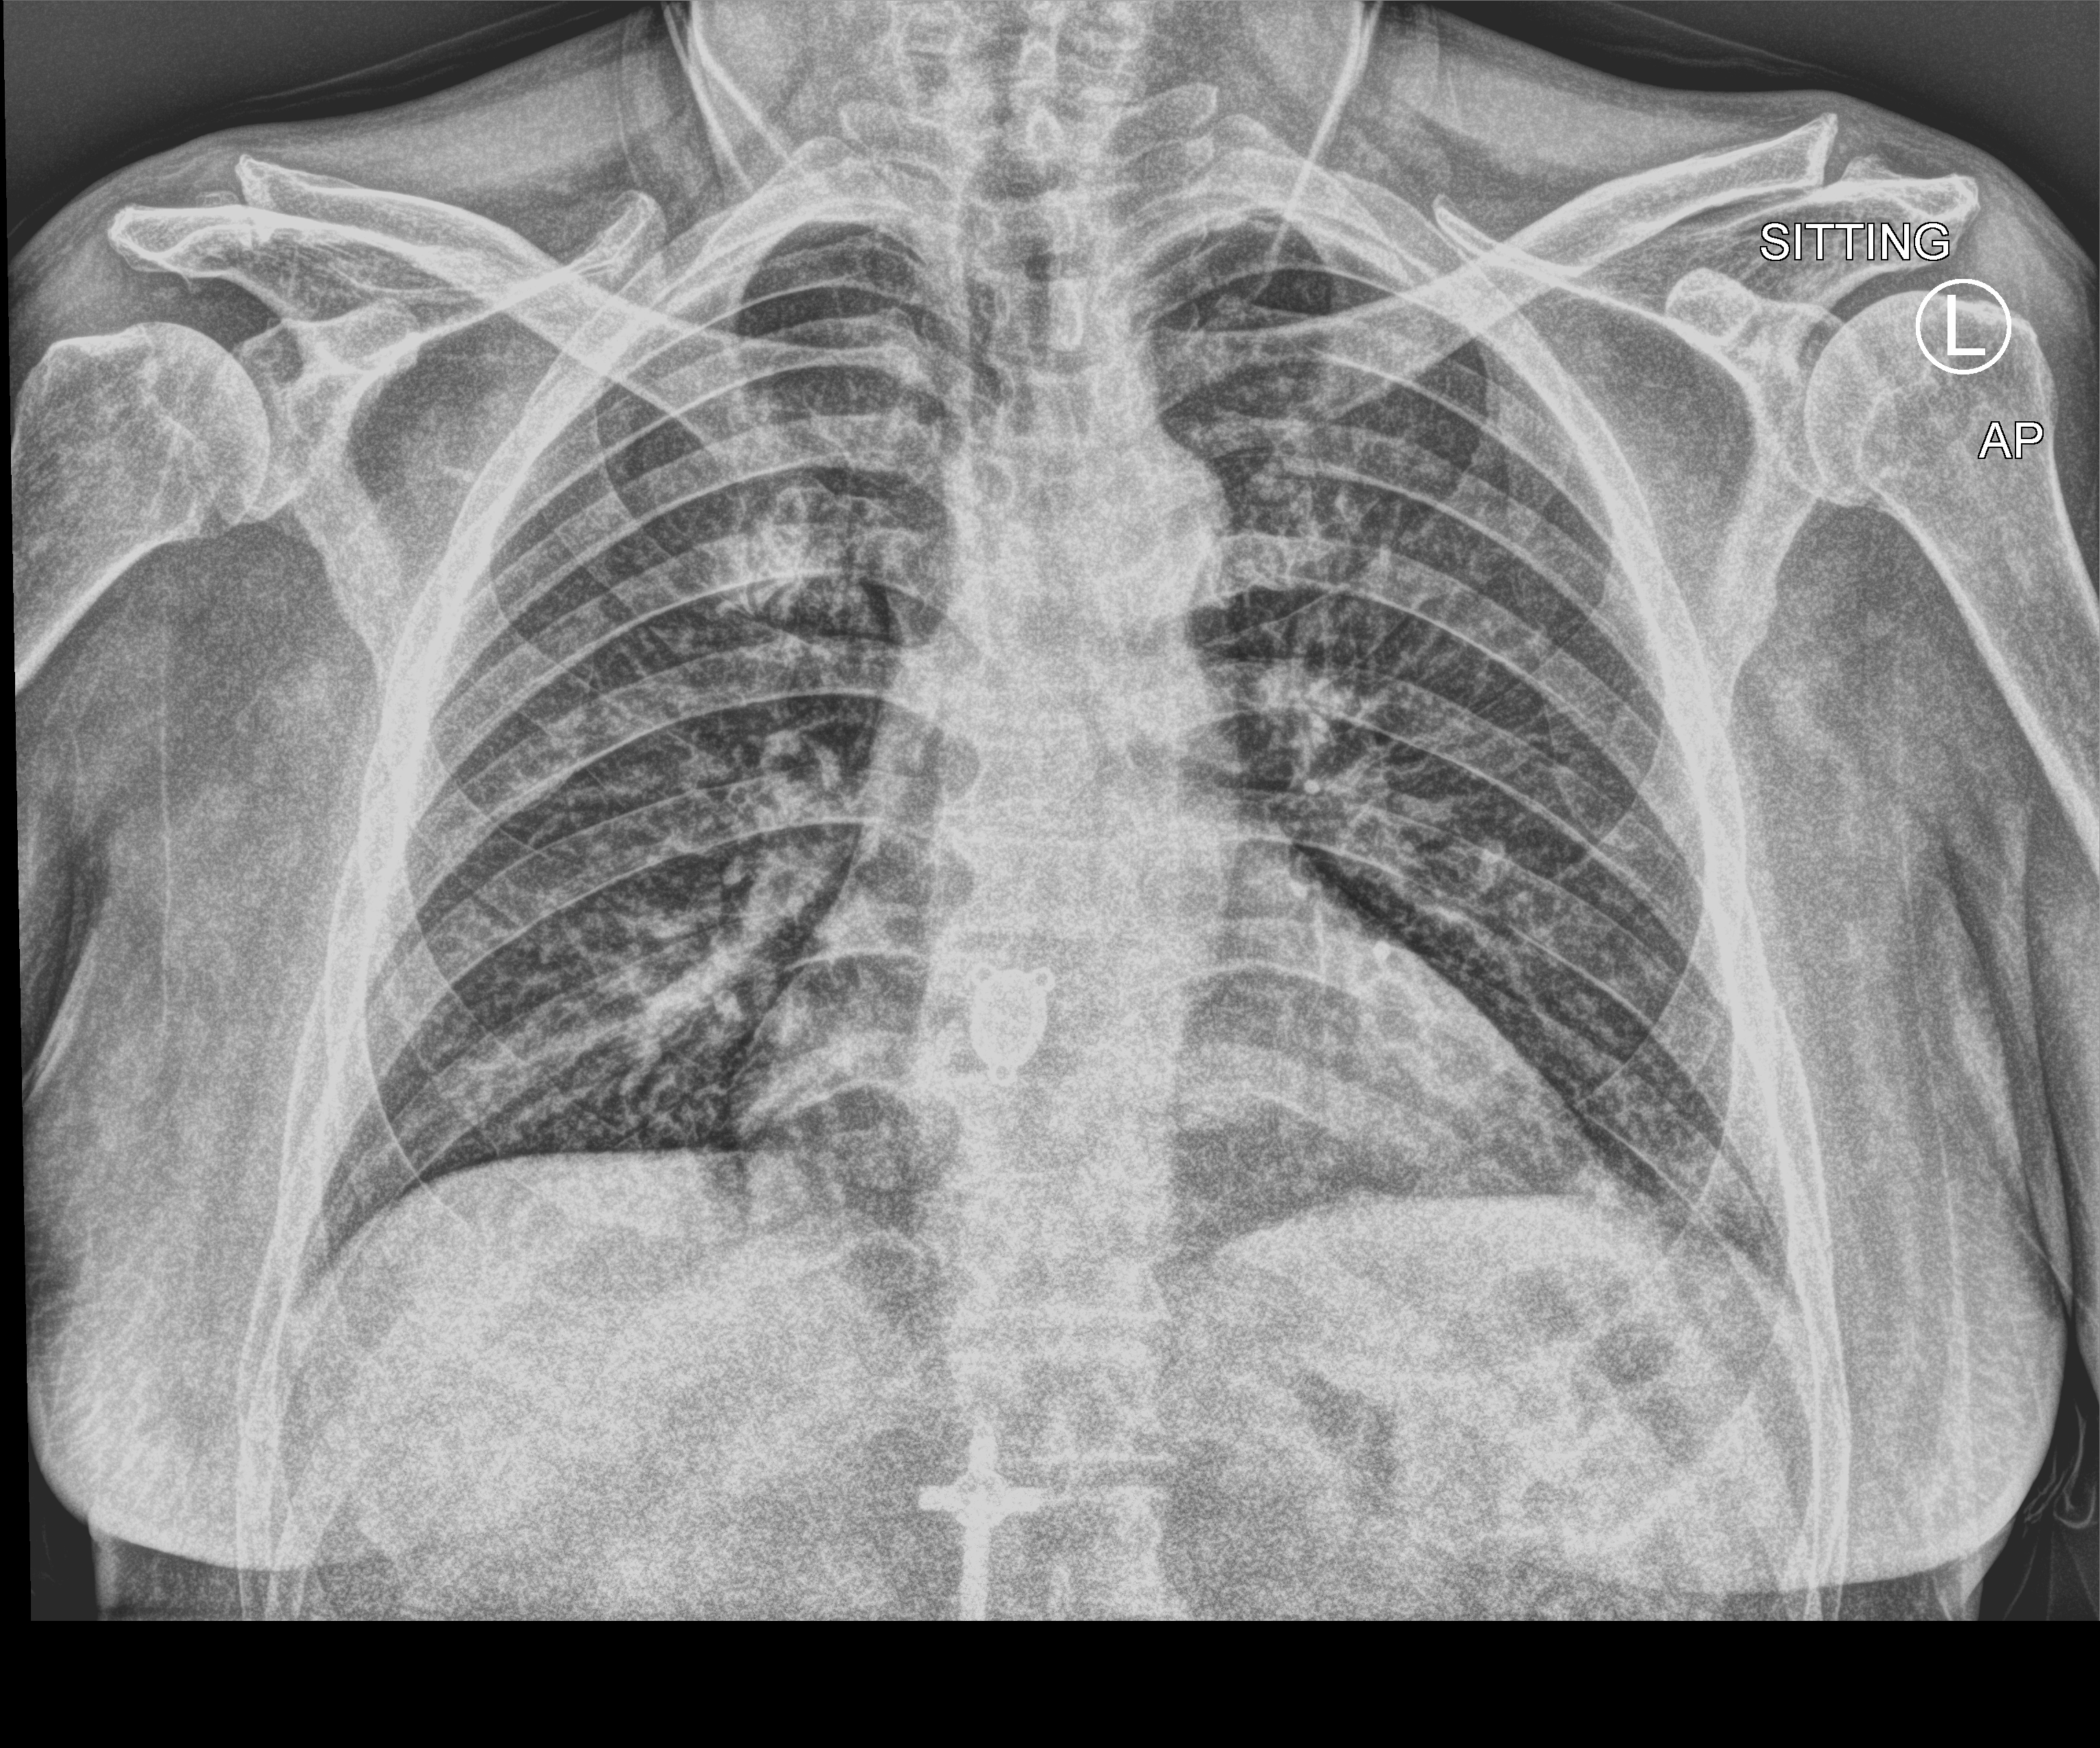
Portable chest radiograph; anteroposterior (AP) projection. Male patient hospitalised with COVID-19, age 18–59 years.
Hospital-stay facts (about this admission, not read from this image; timing relative to this image not recorded): length of hospital stay: 1 day; admitted to intensive care during this hospital stay: no; mechanically ventilated during this hospital stay: no.